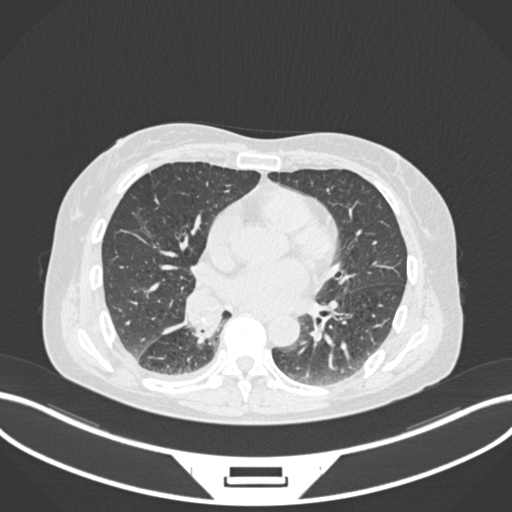
Chest CT, one axial slice. Slice 76 of 168 in the series (ordered by position). Reconstruction kernel B30f. Lung window (W 1500 / L -600 HU). 1 mm slice thickness. 512 × 512 image matrix. Patient: female, 63 years. From the clinical record (not read from this slice): clinical TNM (as recorded): T1c N0 M0.
Outlined on this slice (rectangle marked by the reading radiologist):
- lung tumour (recorded histology: adenocarcinoma): bounding box <192,298,226,344> (left, top, right, bottom; pixels)